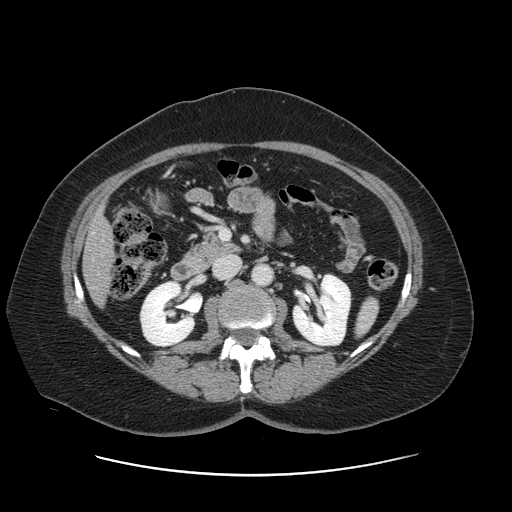
Contrast-enhanced abdominal CT, one axial slice; position 53 of 161 along the scan axis; soft-tissue window (W 400 / L 40 HU); 2.5 mm slice thickness; 512 × 512 image matrix, field of view 398 × 398 mm. Female patient, age 62 years. From the clinical record (not read from this slice): diagnosis: colorectal cancer liver metastases, imaged before liver resection; multiple liver metastases: no; largest metastasis: 2.5 cm; chemotherapy before resection: yes.
Structures marked on this image (outlined manually by an expert reader):
- liver: box from (x=84, y=215) to (x=112, y=303) px